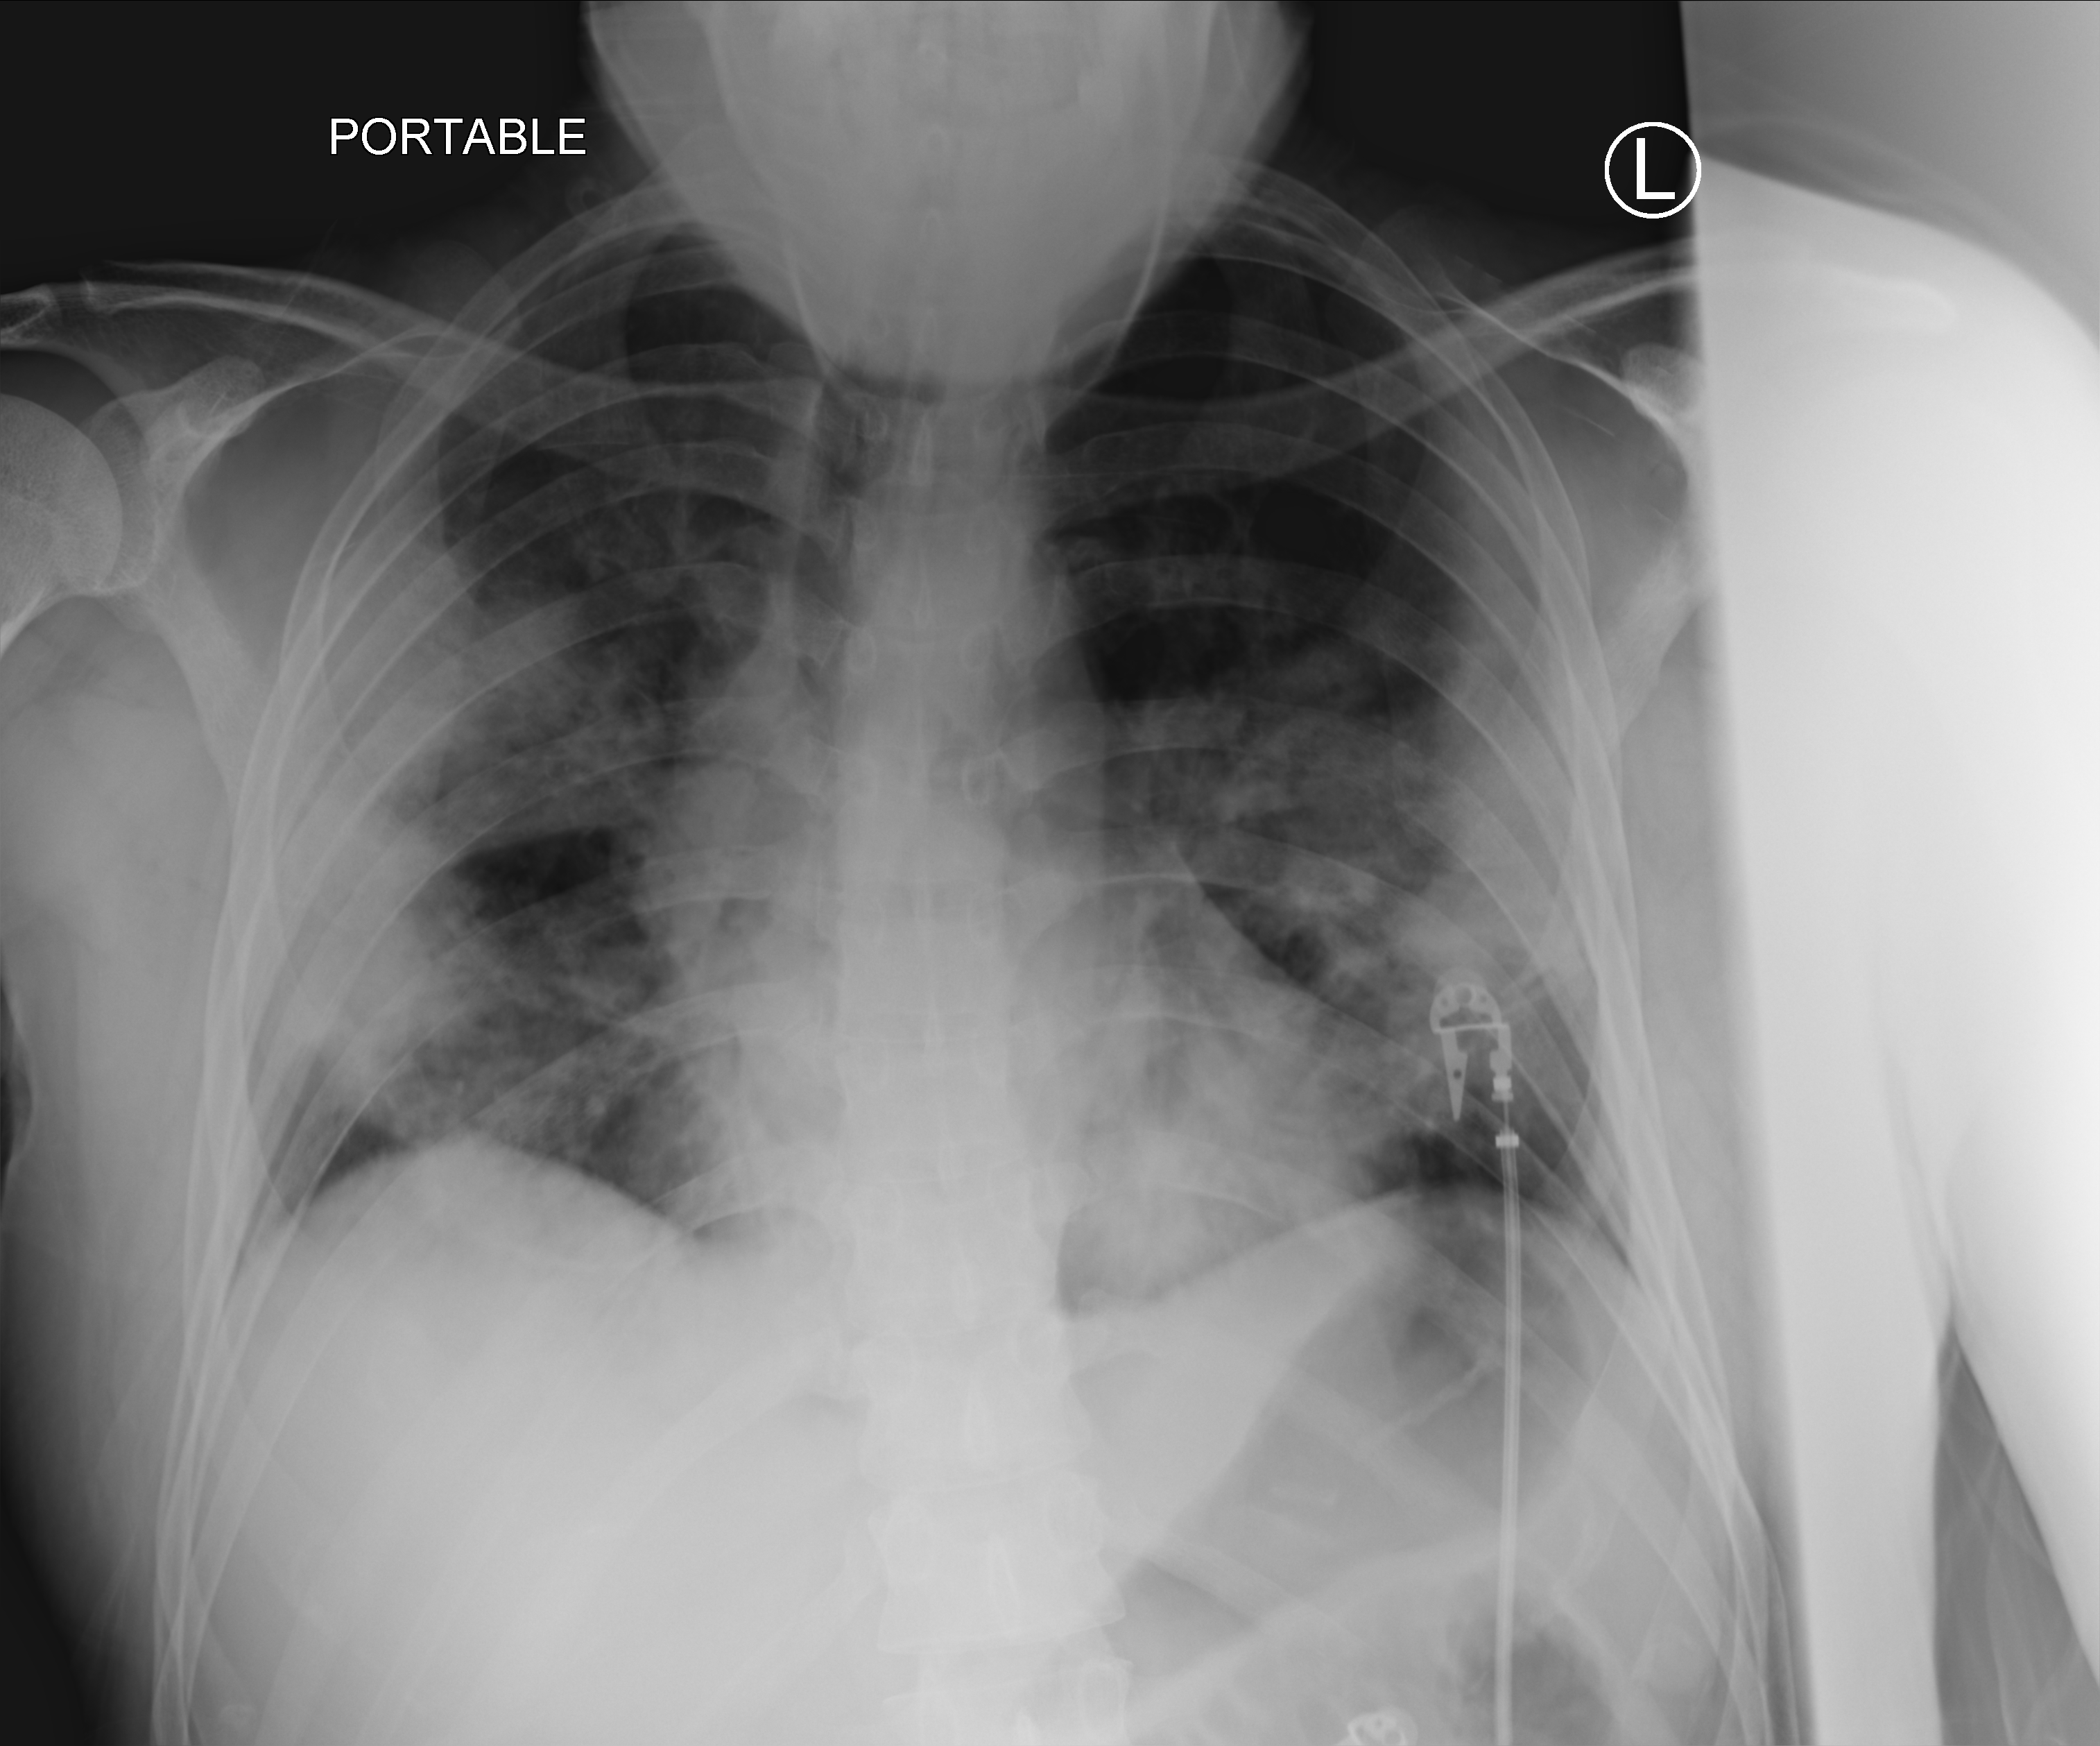
Chest X-ray (portable). Patient hospitalised with COVID-19; male, aged 18–59 years.
Admission-level facts for this patient (not findings on this image; timing relative to this image not recorded): length of hospital stay: 12 days; mechanically ventilated during this hospital stay: no.